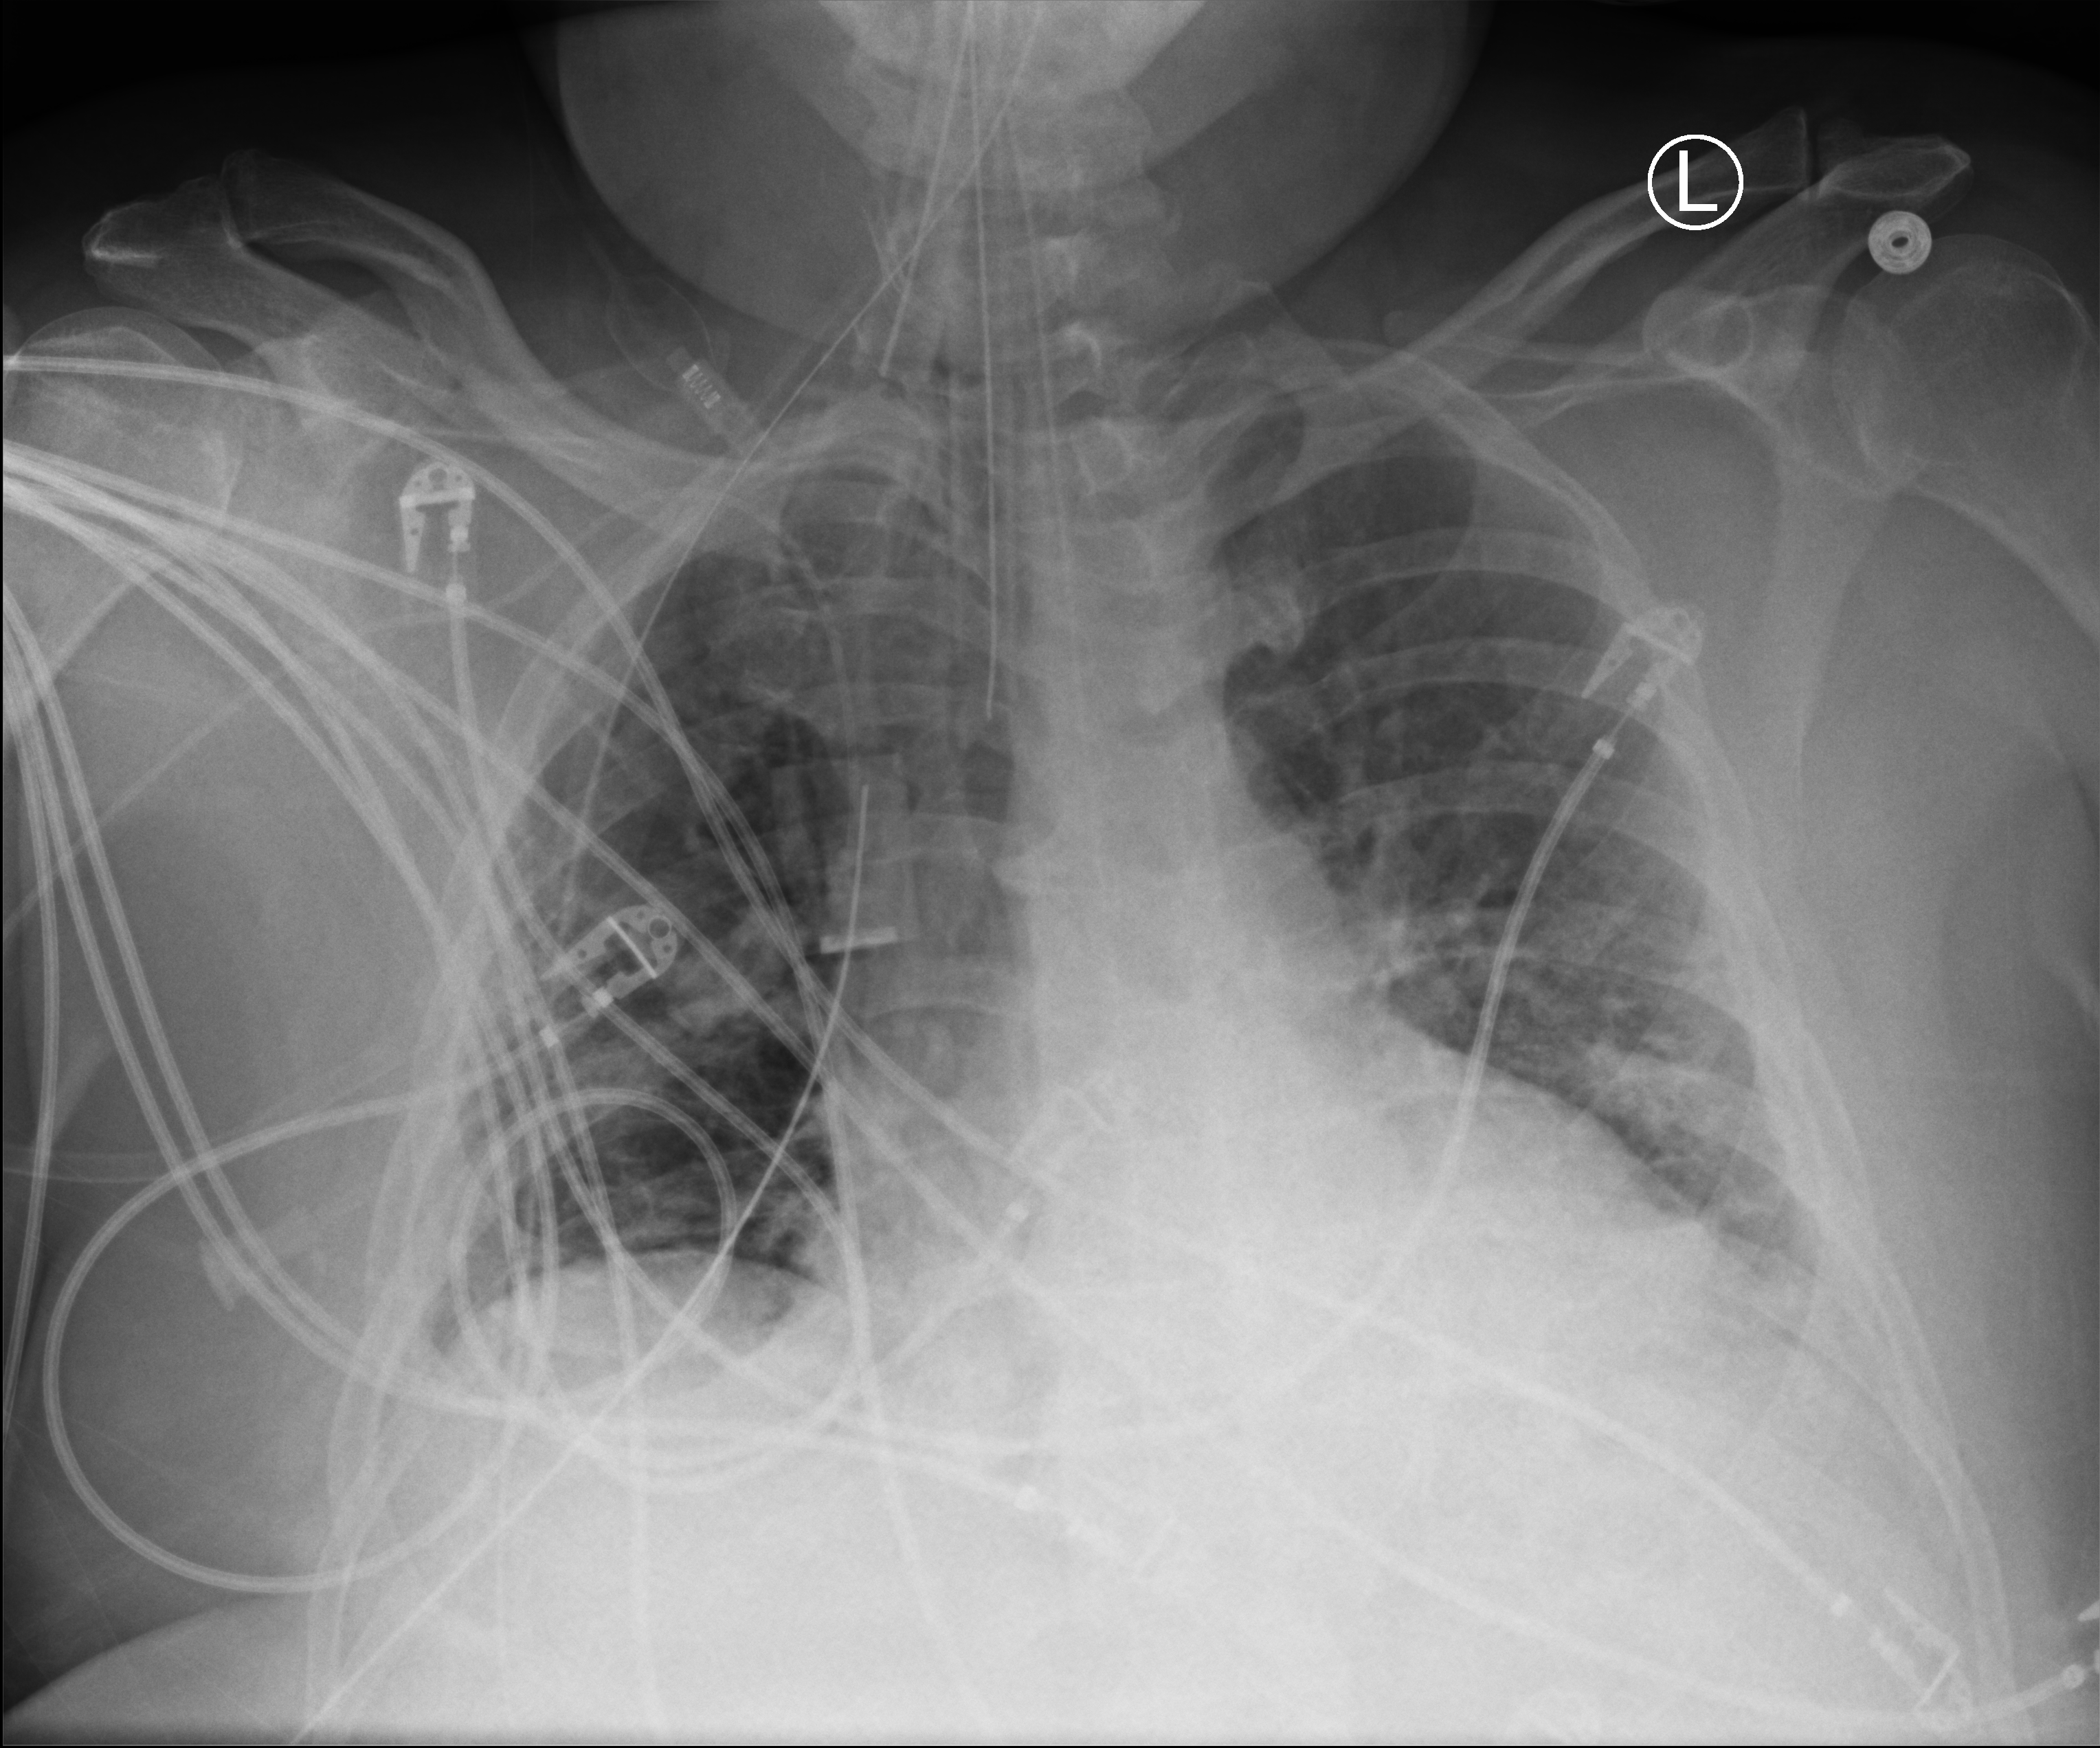
Bedside chest radiograph (computed radiography); anteroposterior (AP) projection. Patient hospitalised with COVID-19; male, aged 18–59 years.
Admission-level facts for this patient (not findings on this image; timing relative to this image not recorded):
- diabetes (admission record): no